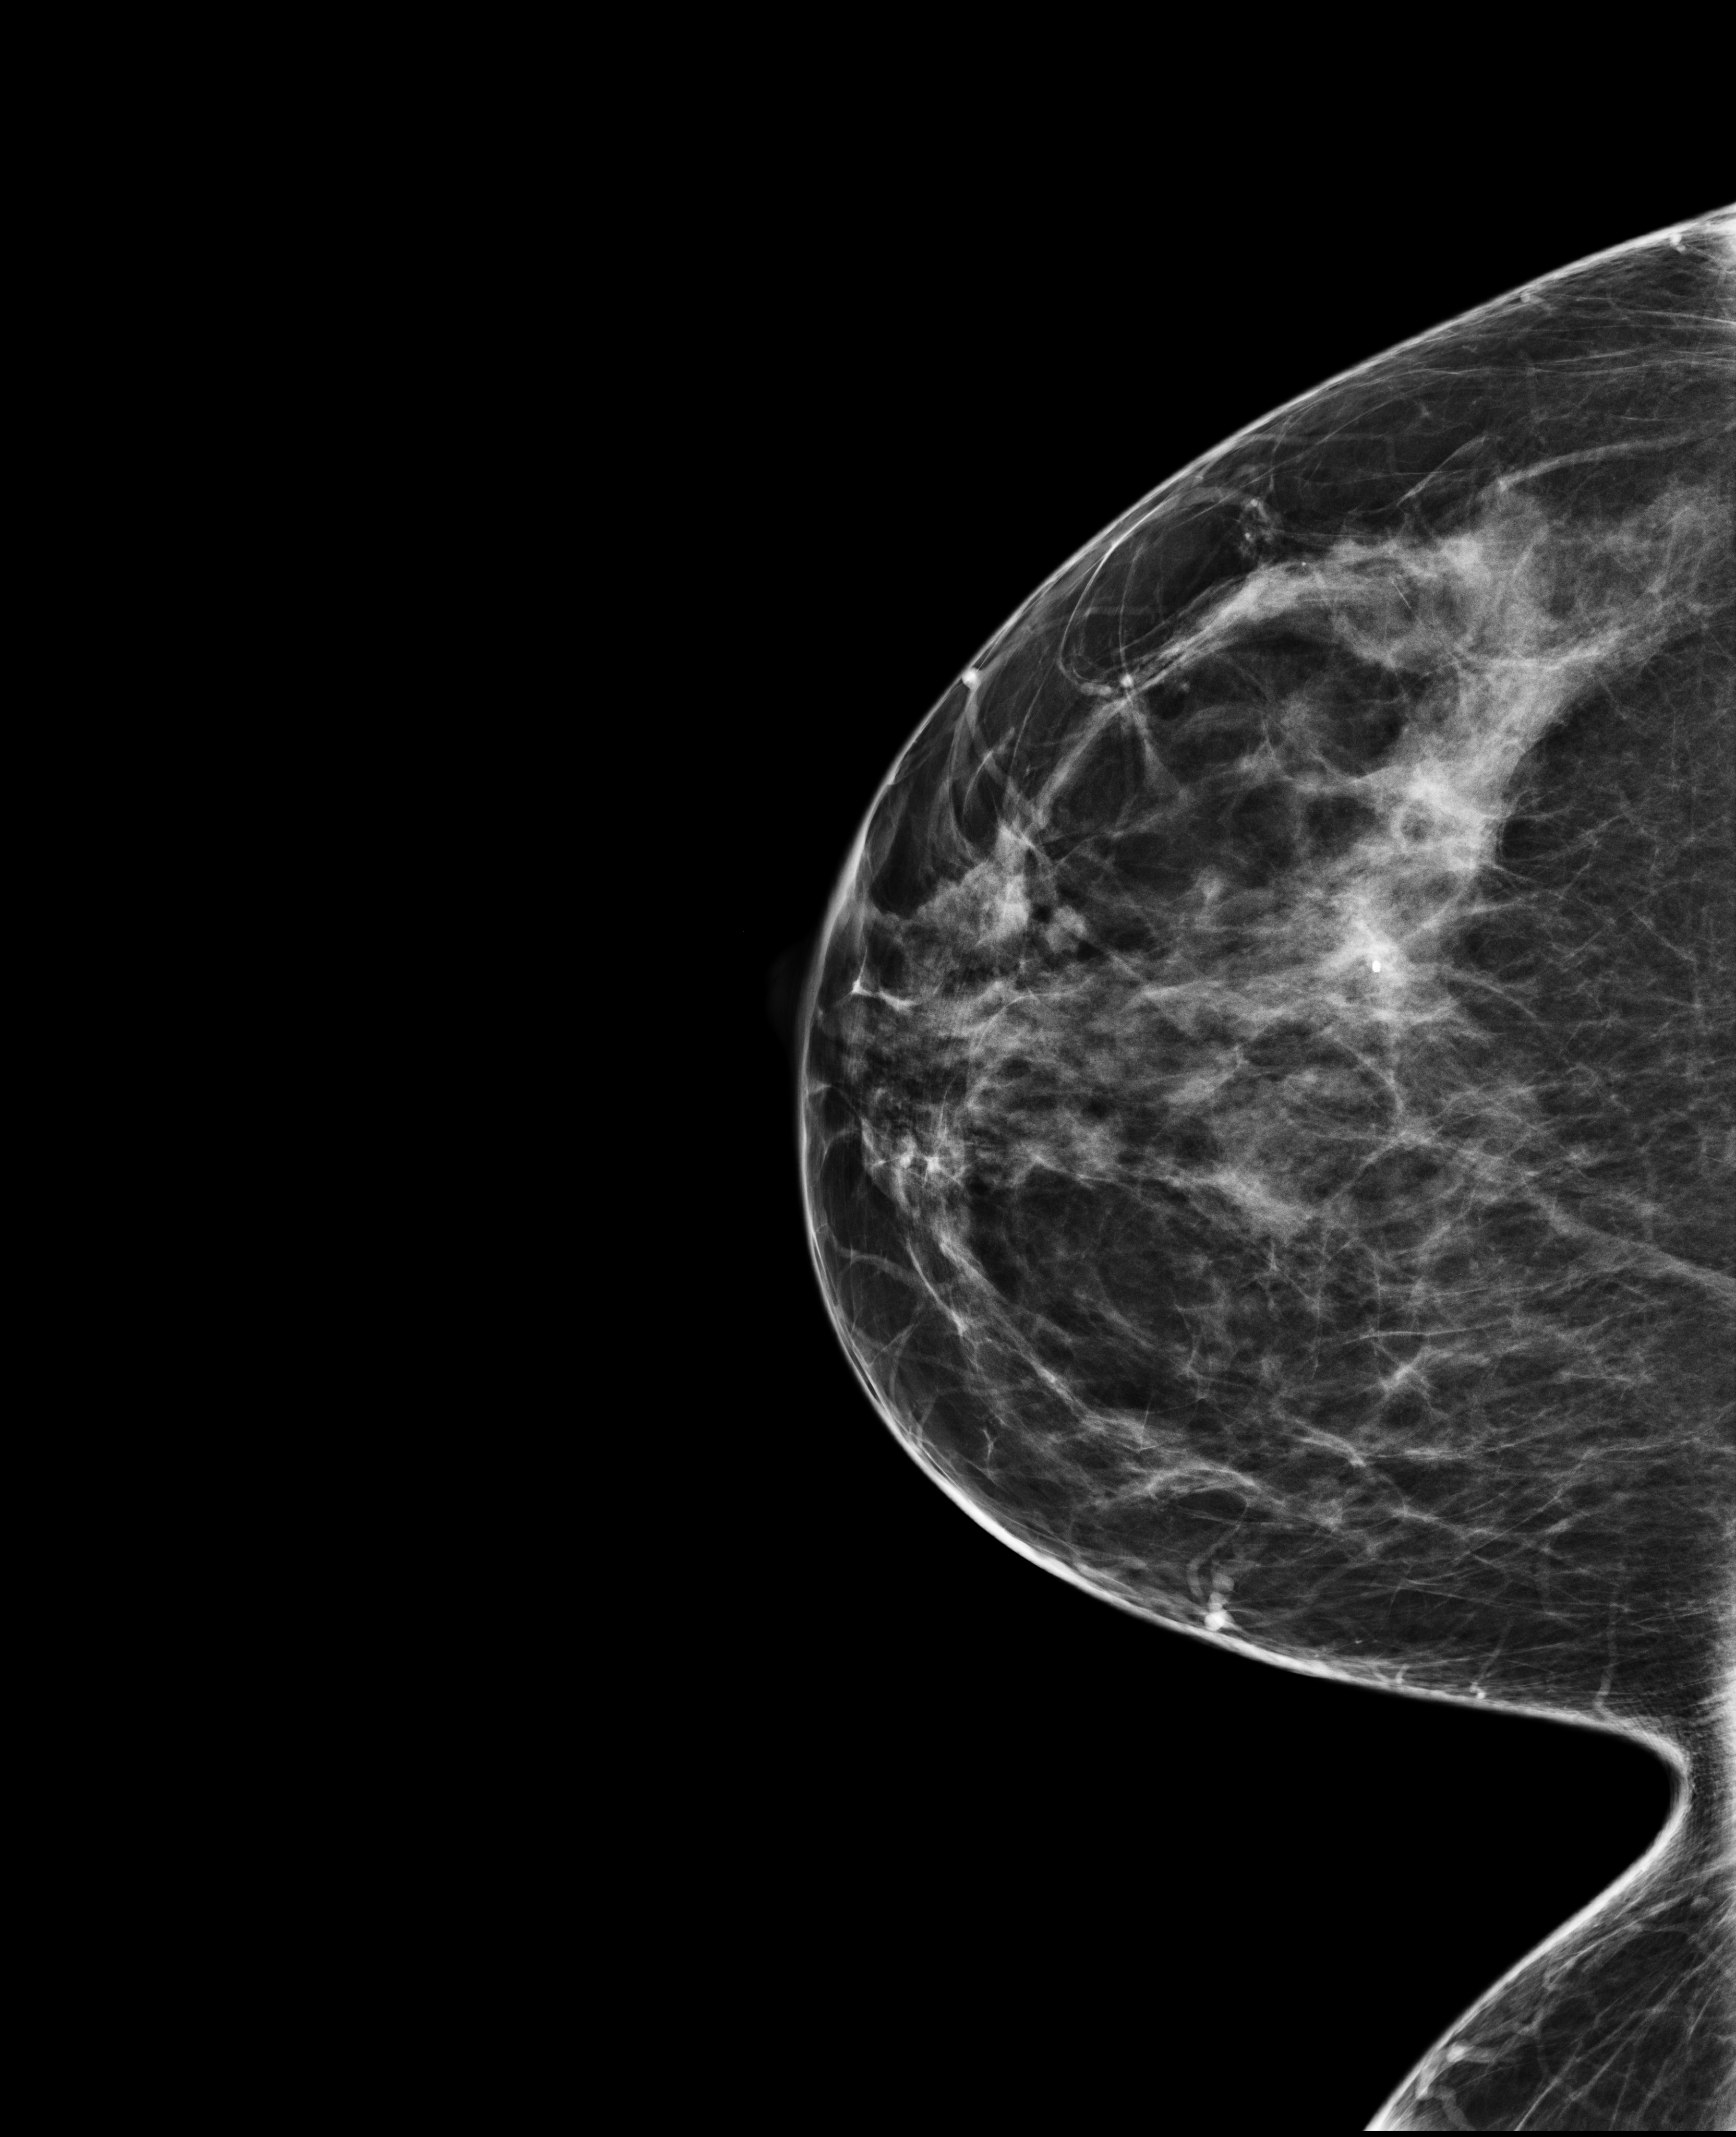
Digital mammogram (FFDM); right breast; cranio-caudal projection; annual screening mammography examination; compressed breast thickness 69 mm. Patient: female, 47 years.
- breast density at the screening exam (both breasts): heterogeneously dense (BI-RADS density category c)
- final BI-RADS category for the screening round (tomosynthesis exam, both breasts): category 2
- recall: no recall after this screen